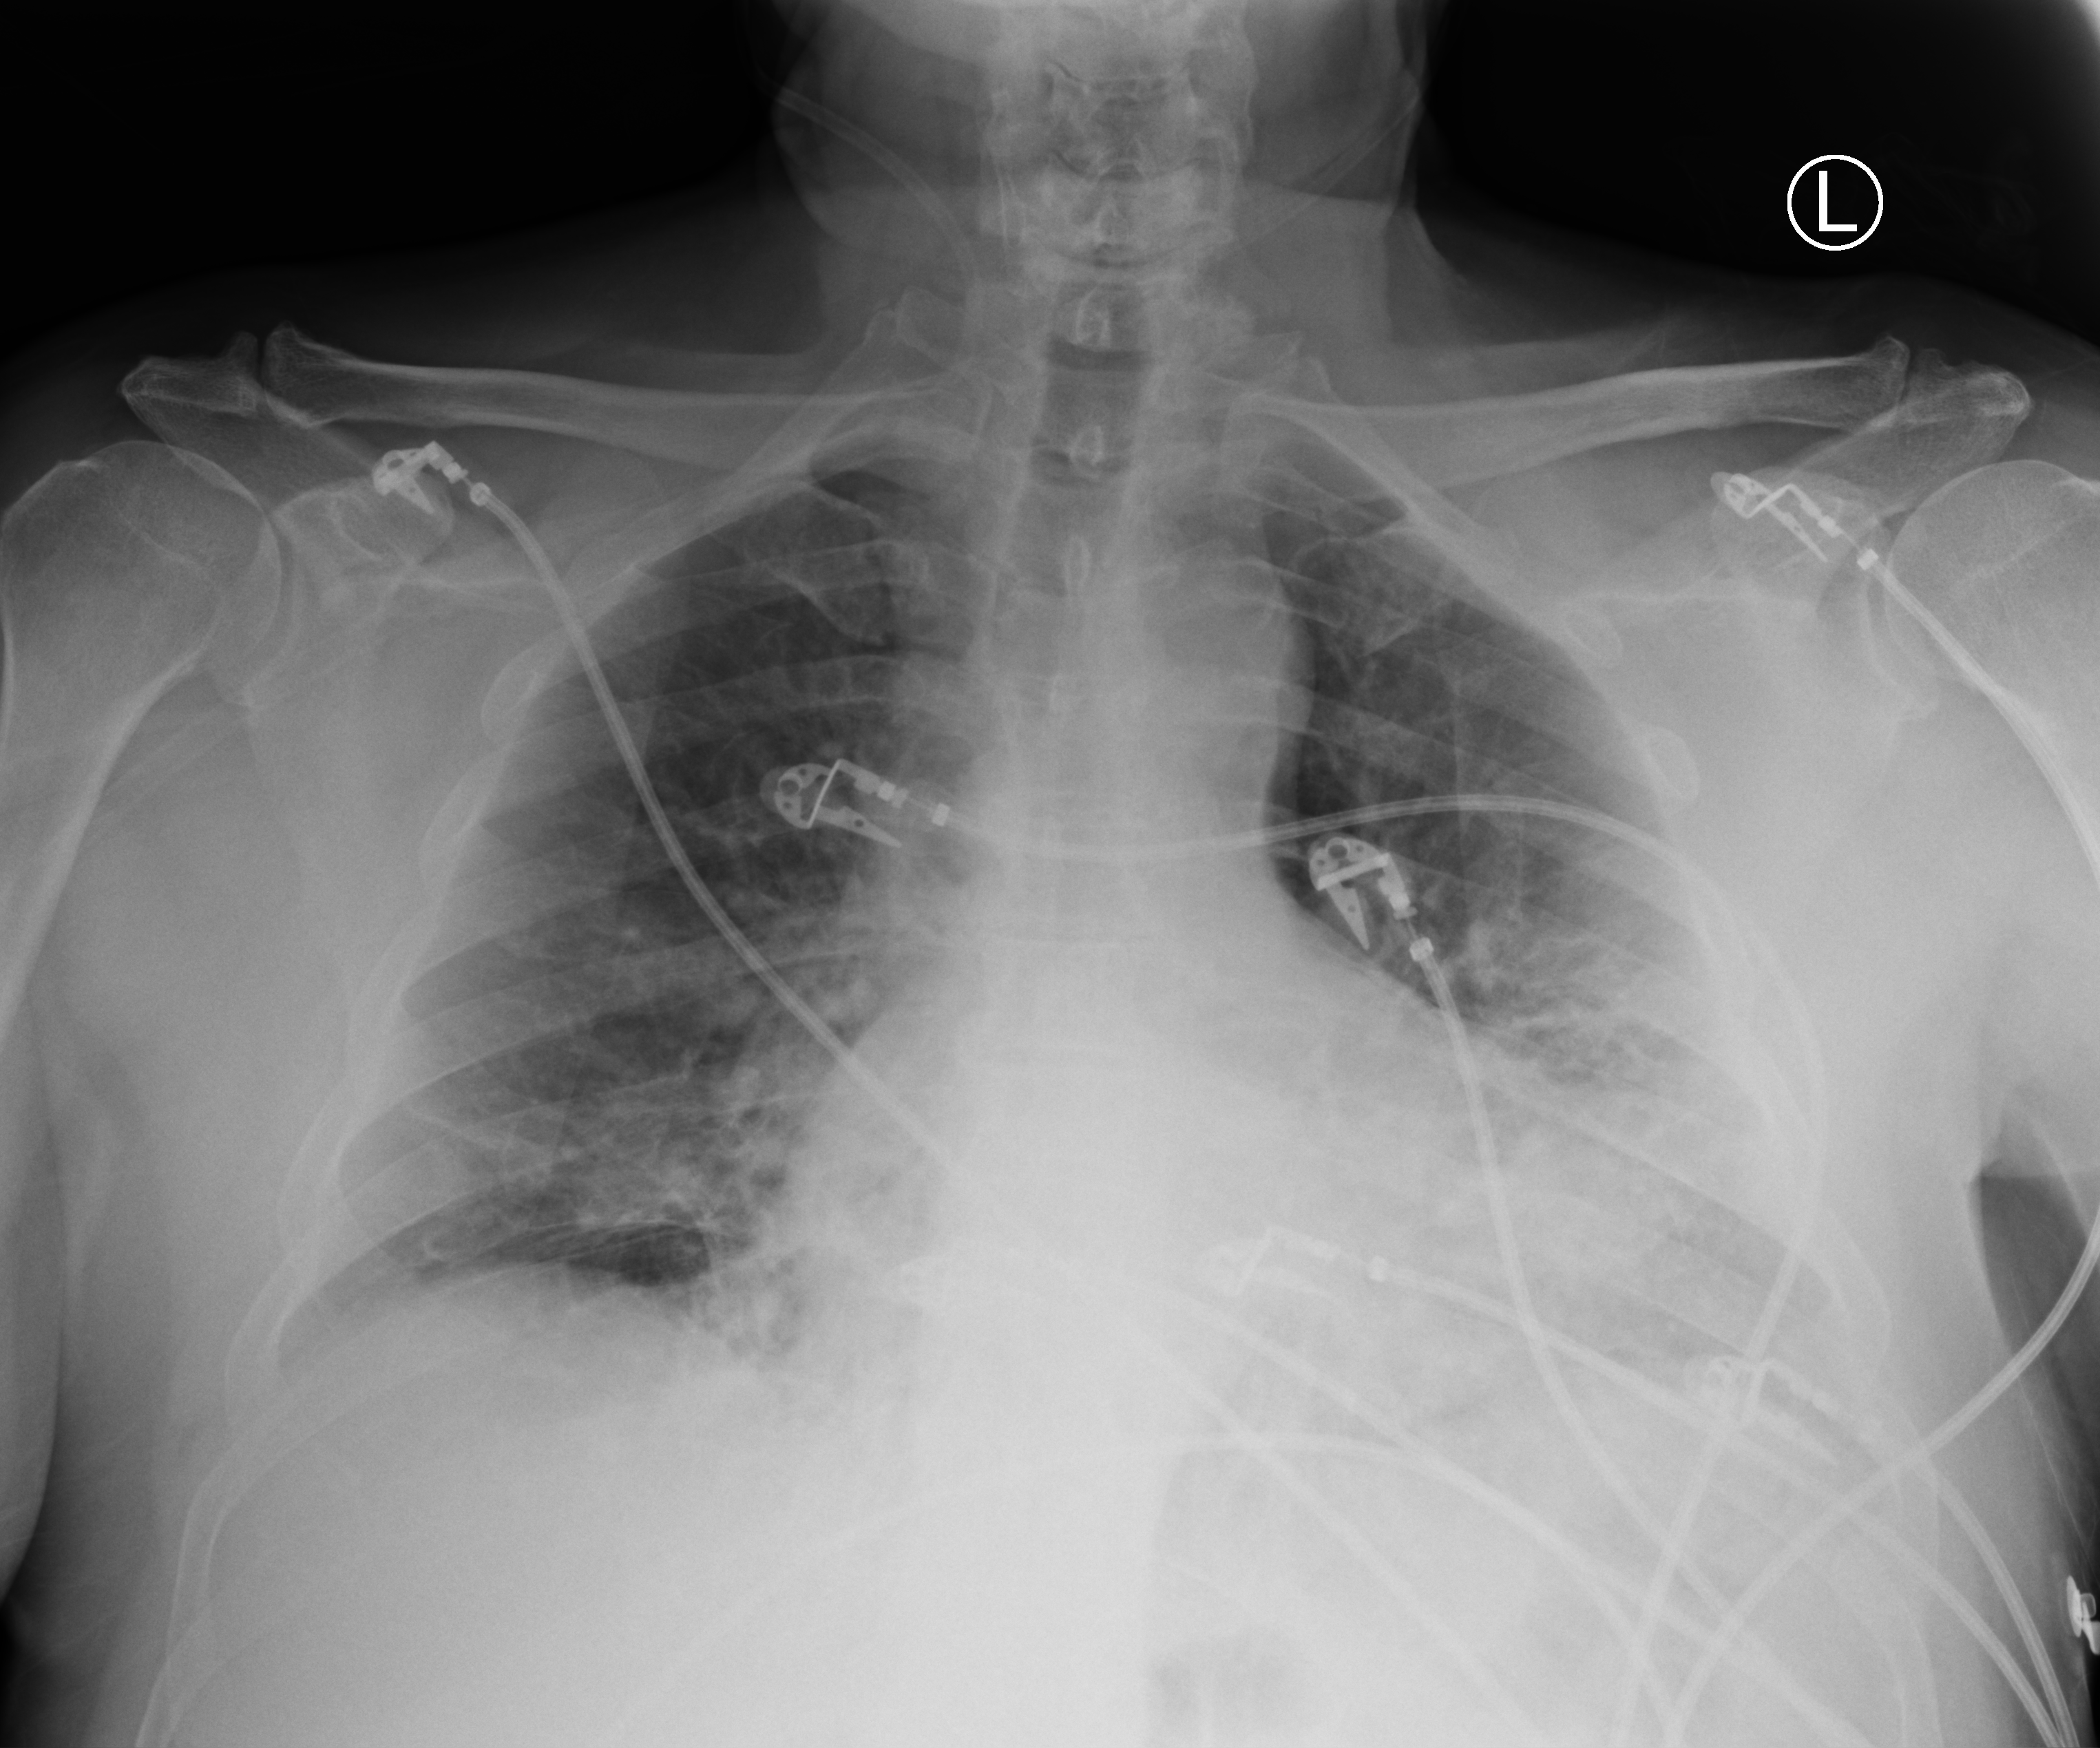
Chest X-ray (portable); anteroposterior (AP) projection. Patient hospitalised with COVID-19; male, aged 60–74 years.
From the hospital-stay record, not from the radiograph (when in the stay this image was taken is not recorded):
- chronic kidney disease (admission record): no
- COPD (admission record): no